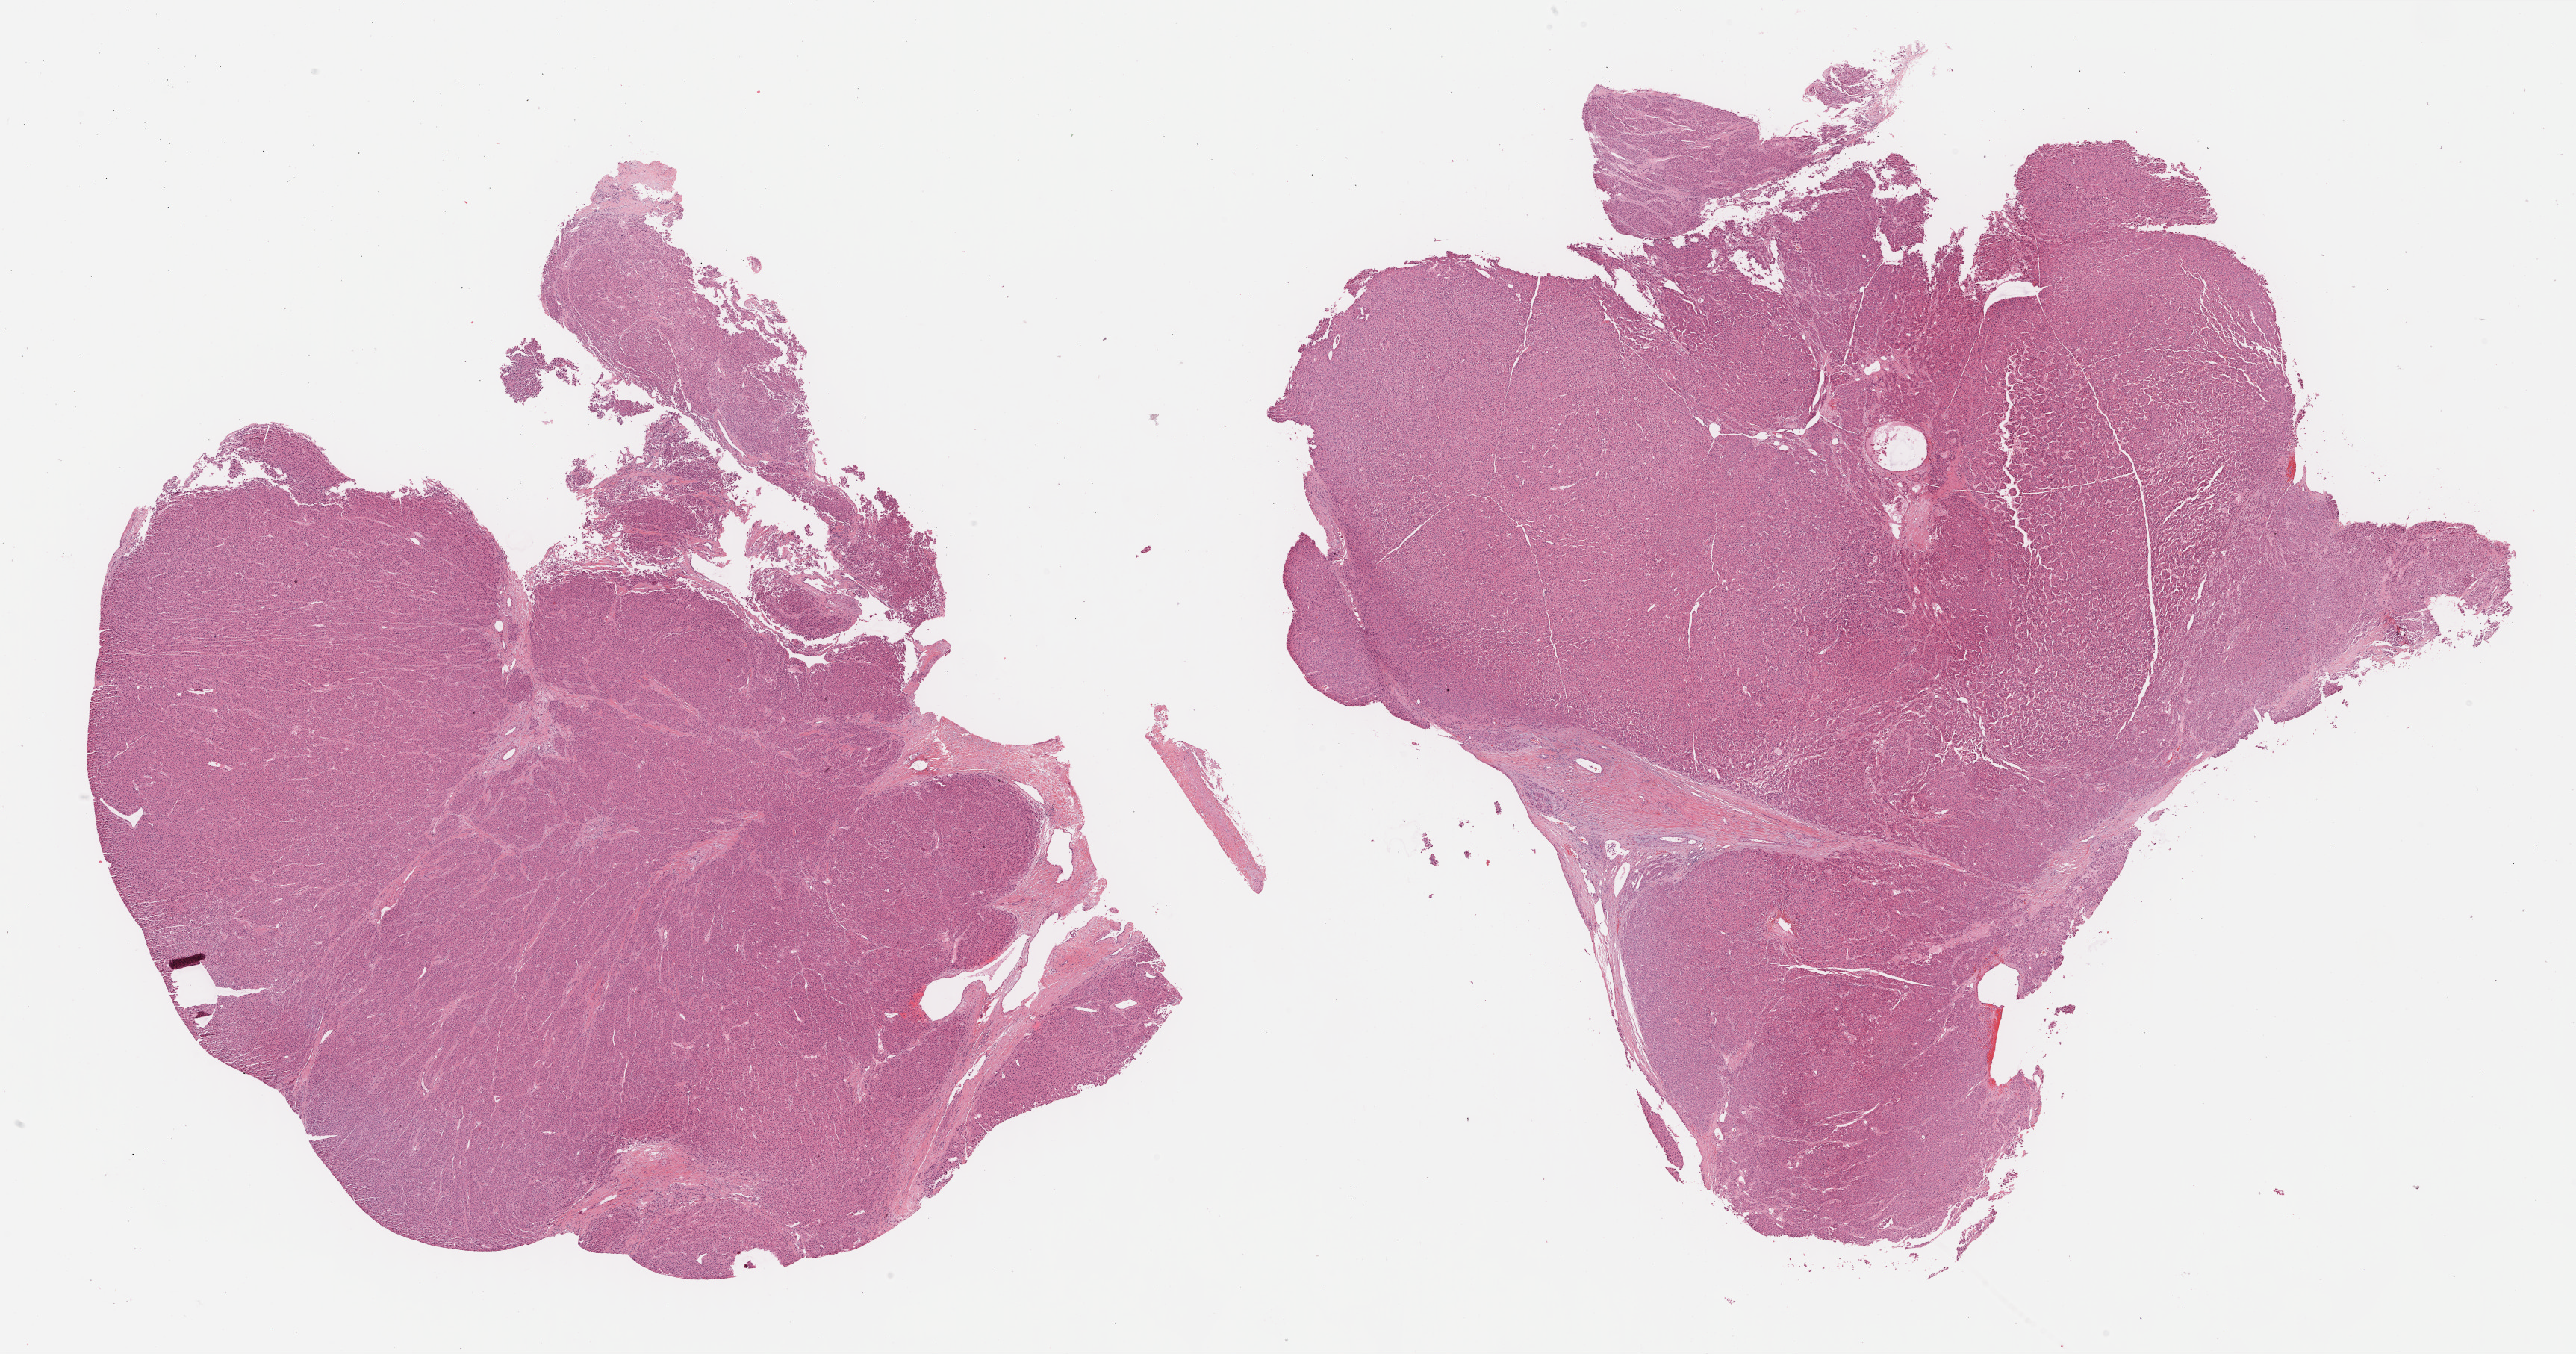
Digitized Hematoxylin and eosin (H&E) stained tissue section (whole slide), whole scanned area (about 27.9 x 14.7 mm, acquisition: 40x scan) shown as a low-resolution overview. FFPE section. Liver, primary tumour sample. Female patient; age at initial diagnosis 66 years.
Histologic diagnosis: Hepatocellular carcinoma, NOS.